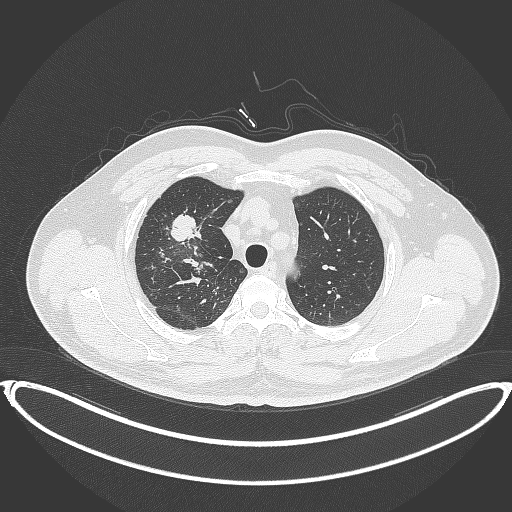
Chest CT, one axial slice; slice 306 of 399 in the series (ordered by position); 120 kVp; lung window (W 1500 / L -600 HU); 512 × 512 image matrix, field of view 445 × 445 mm. Patient: male, 53 years. Case-level facts recorded for this patient, not image findings: clinical TNM (as recorded): T2a N0 M0.
Structures marked on this image (bounding box drawn by a radiologist):
- lung tumour (recorded histology: adenocarcinoma): bounding box <167,212,200,249> (left, top, right, bottom; pixels)